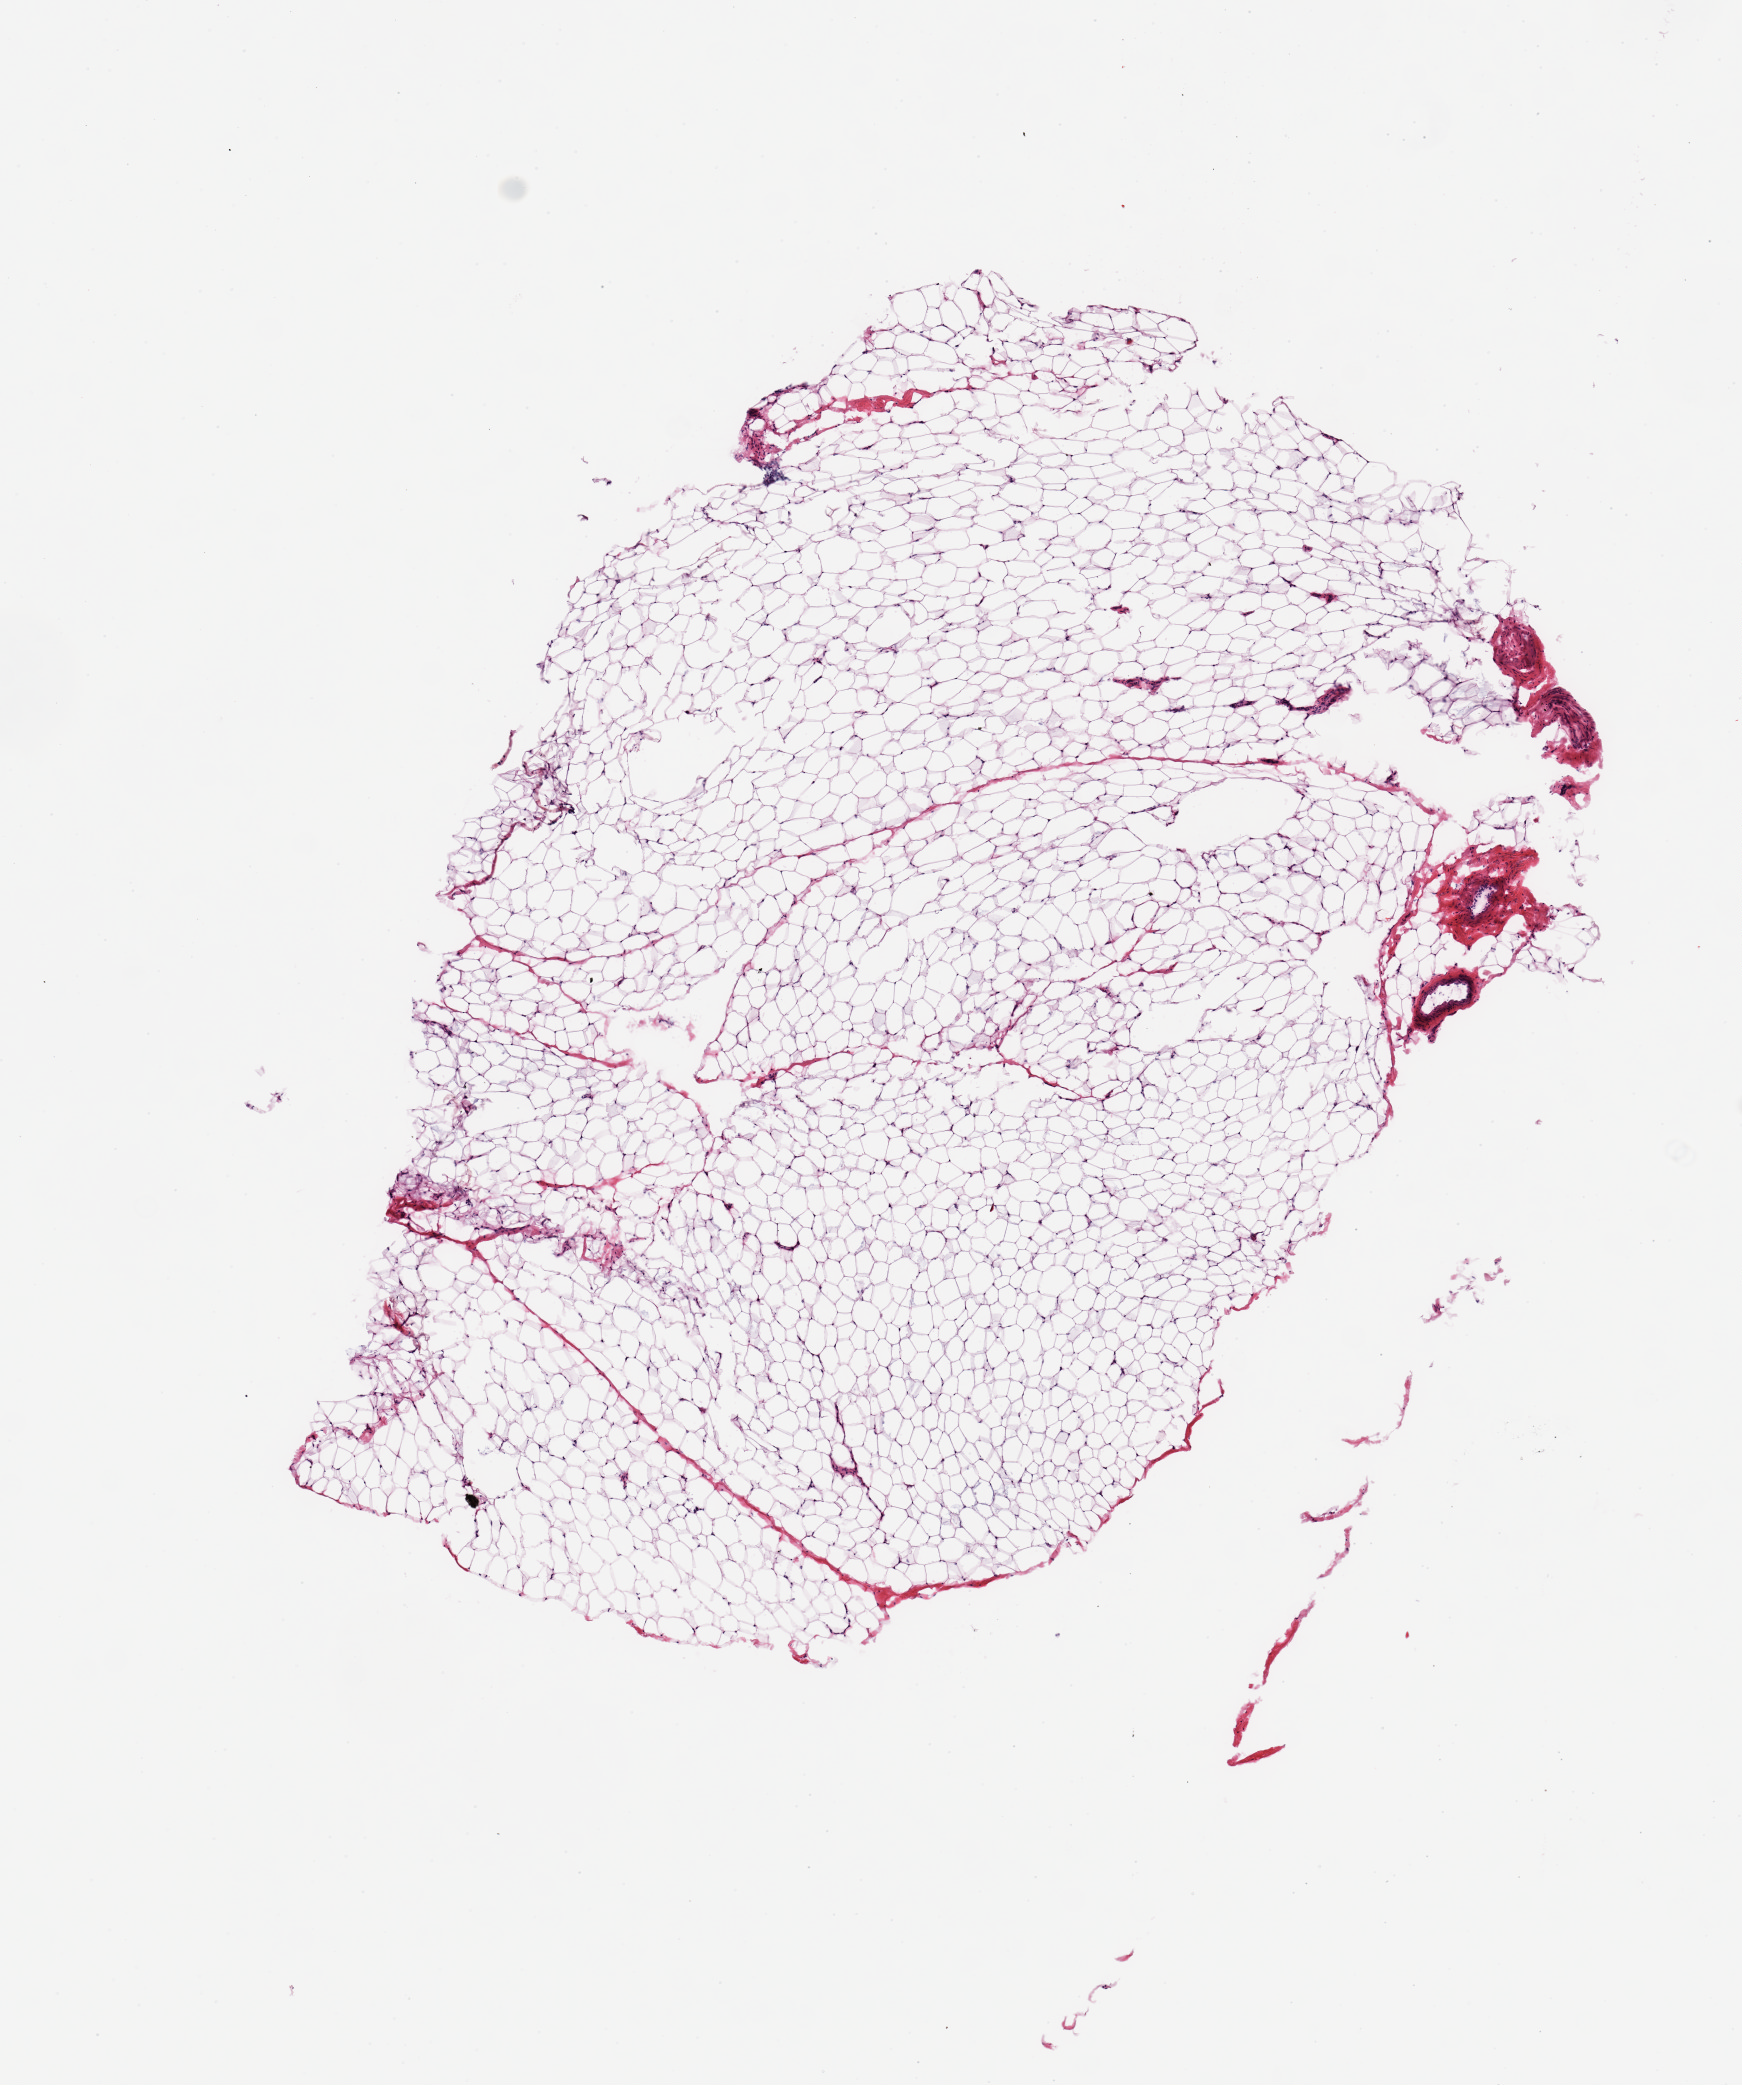
Digitized H&E-stained section — whole scanned area (about 6.9 x 8.2 mm) shown as a low-resolution overview.
• specimen: frozen section (dry ice); section of breast (target tissue); tissue donor sample